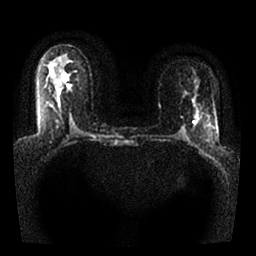
Breast MRI, one axial slice. Slice 17 of 25 in the series (ordered by position). Diffusion-weighted series; image 2 of 4 stored at this slice position (different b-values; order by instance number). 1.5 T. 4 mm slice thickness. 256 × 256 image matrix, field of view 330 × 330 mm. Female patient.
Structures marked on this image (outlined manually by an expert reader):
- tumour on diffusion-weighted imaging: bounding box [x1, y1, x2, y2] px = [67, 84, 72, 88]